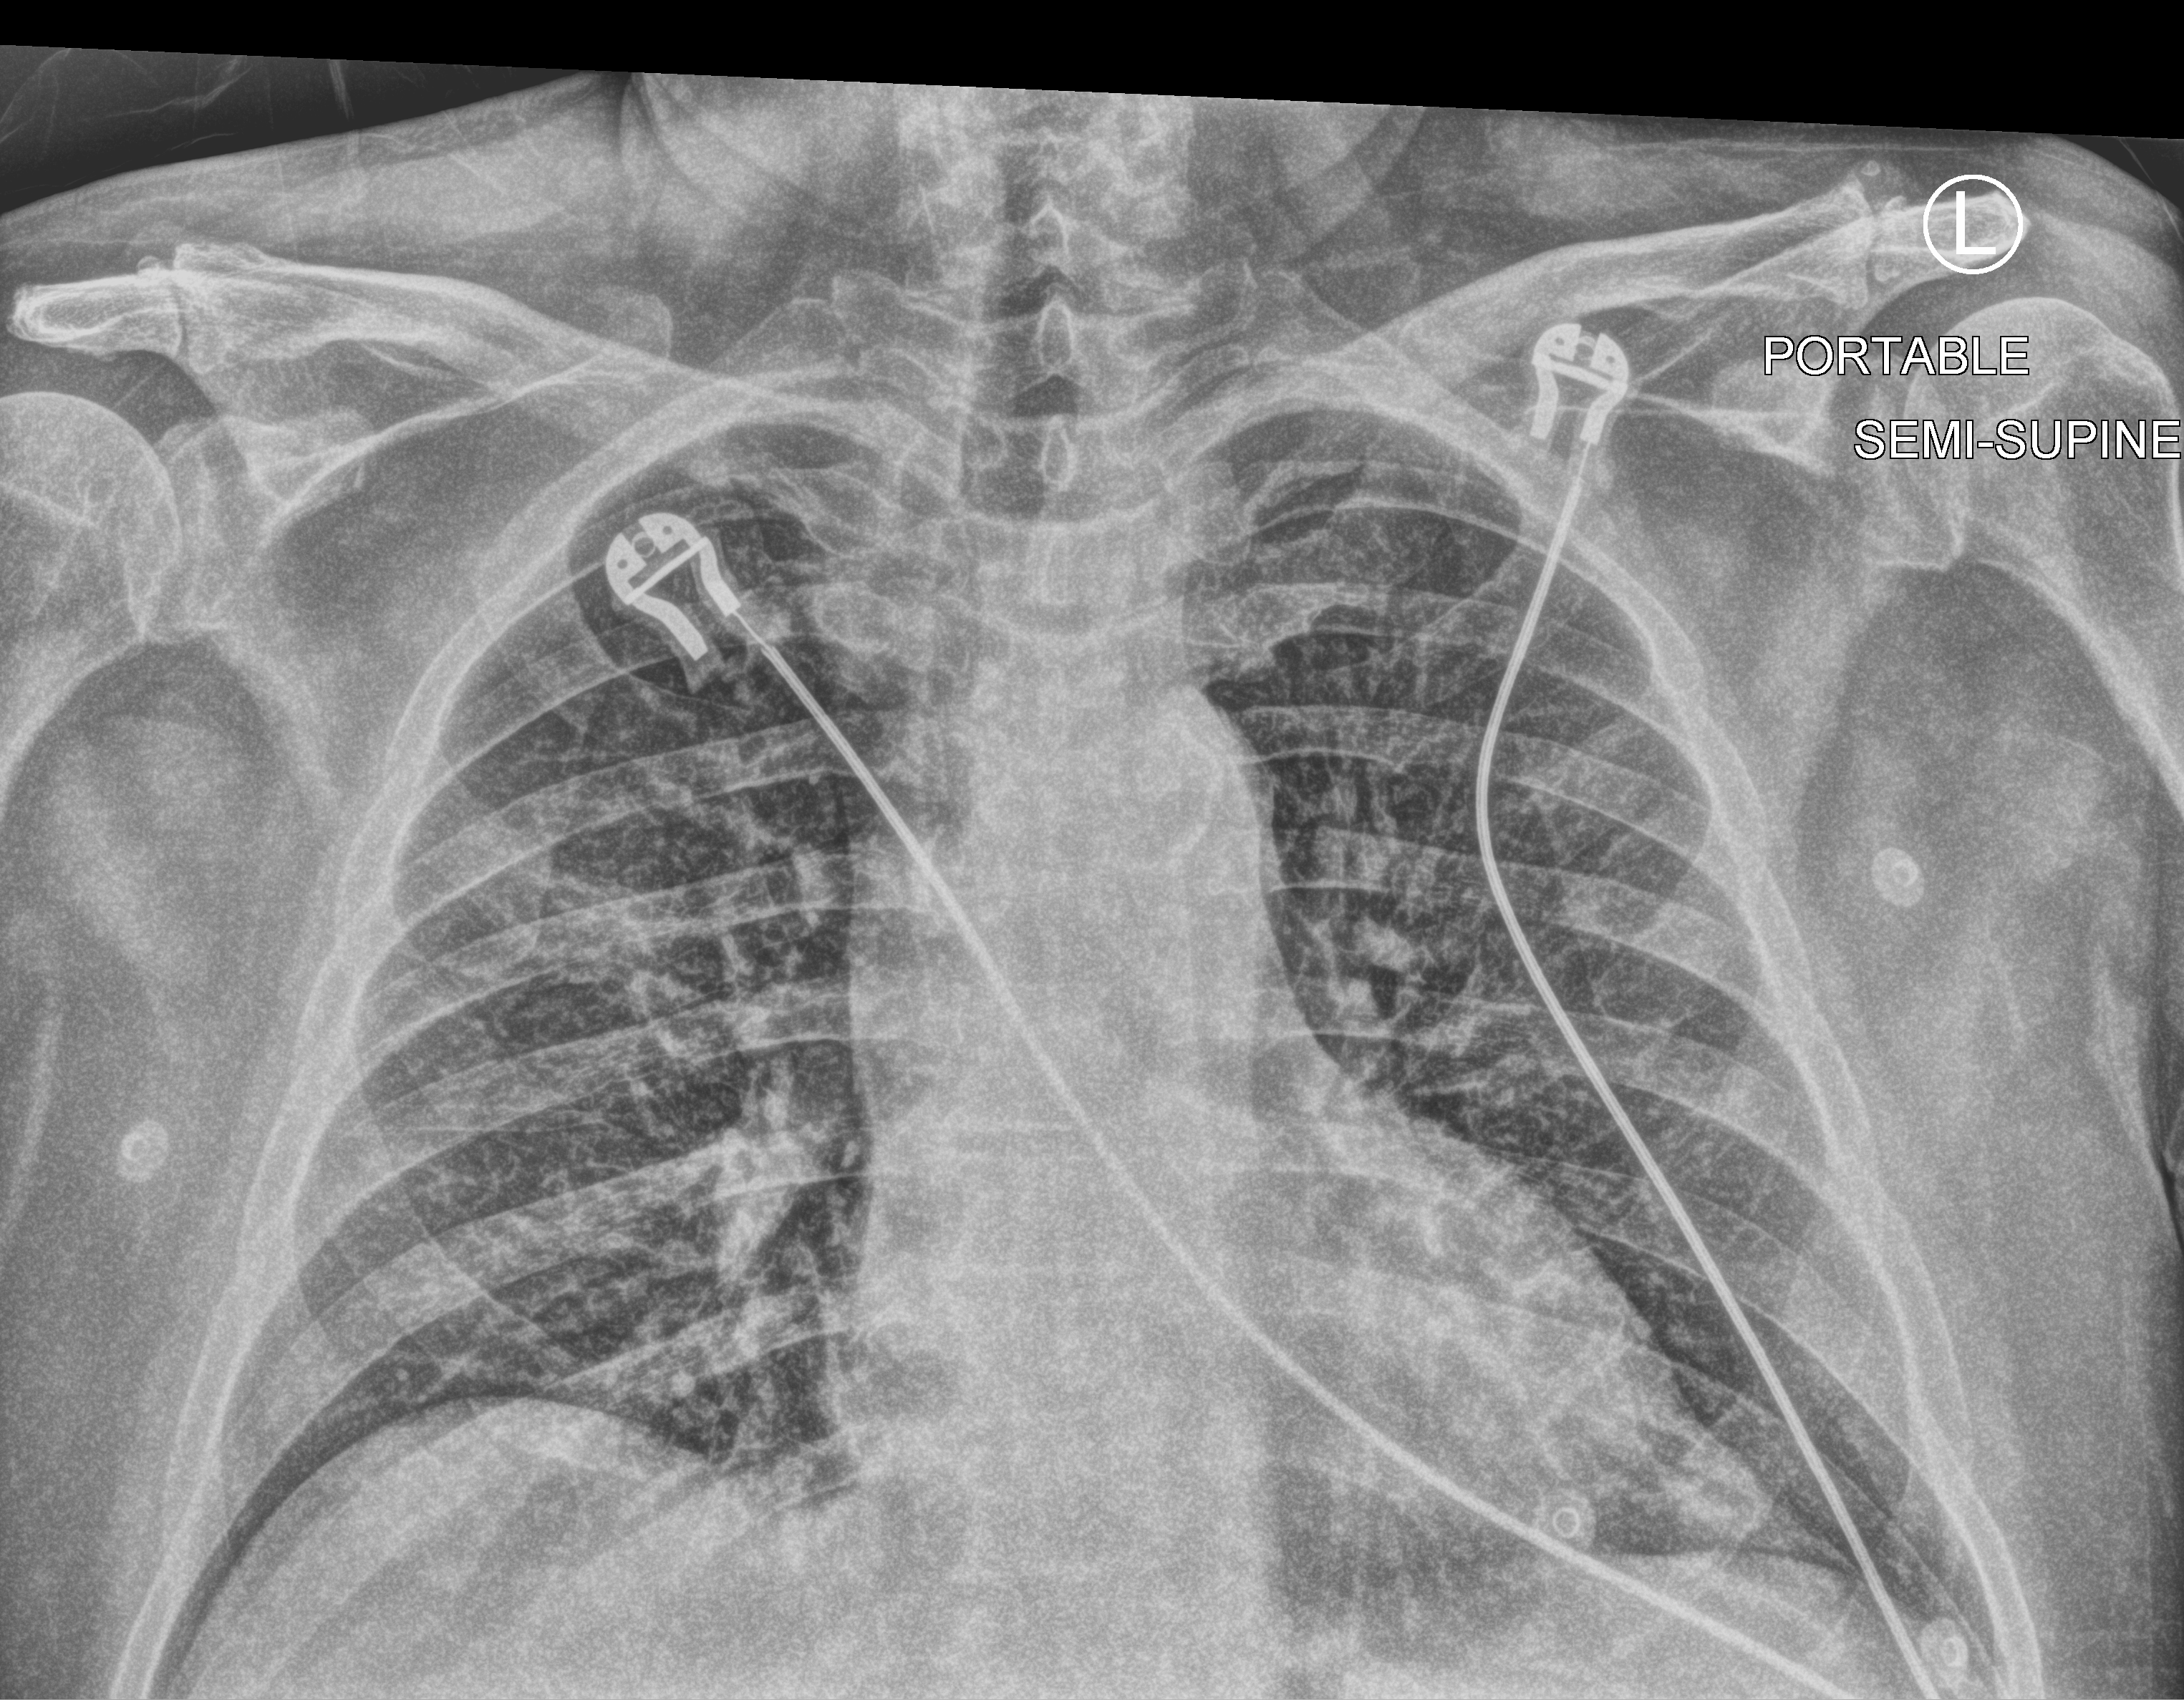
Chest X-ray (portable); anteroposterior (AP) projection. Male patient hospitalised with COVID-19, age 60–74 years.
Hospital-stay facts (about this admission, not read from this image; timing relative to this image not recorded): mechanically ventilated during this hospital stay: no; admitted to intensive care during this hospital stay: no.